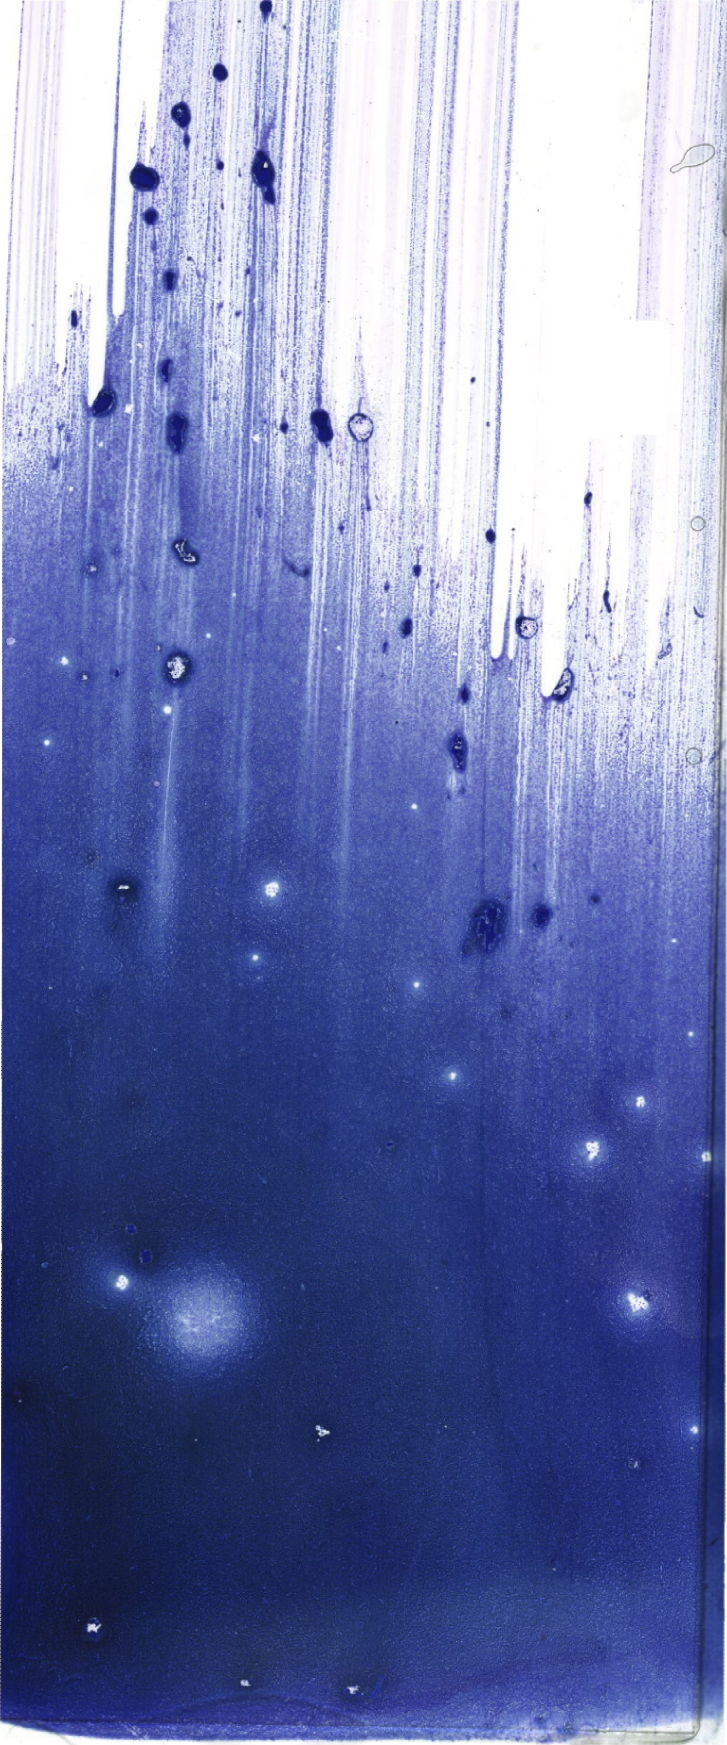
Whole-slide image of a May-Grünwald–Giemsa-stained bone marrow aspirate smear — low-resolution overview of the scanned area, about 20.6 x 49.5 mm. Patient sex: male.
* diagnosis: Acute Myeloid Leukemia with Maturation